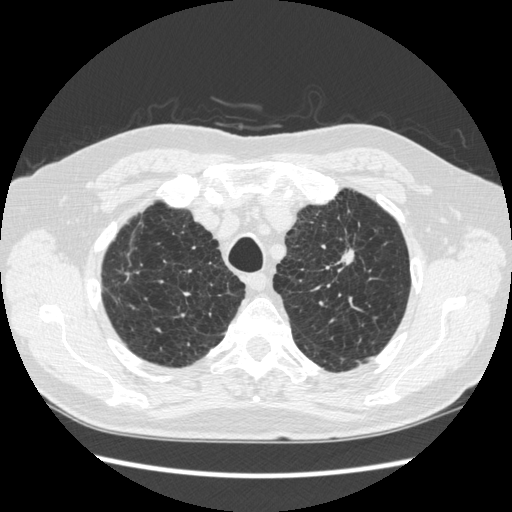
Chest CT (low-dose screening protocol), one axial image; third annual screen; lung window (W 1500 / L -600 HU); 1.25 mm slice thickness; 120 kVp; slice 48 of 267 in the series; 512 × 512 image matrix, field of view 360 × 360 mm. Male, age 70 years at enrolment. Former smoker at enrolment.
Lesion marked by an expert reader, bounding box [x1, y1, x2, y2] px = [323, 215, 373, 280]. The screening reader recorded 2 non-calcified nodules or masses ≥4 mm on this exam (left upper lobe, right lower lobe); which of them this box marks is not recorded. Official screen result: positive, other. Lung cancer was diagnosed 92 days after this screen: squamous cell carcinoma, NOS, left upper lobe, moderately differentiated (G2), stage IA (AJCC 6th edition), 18 mm at pathology.